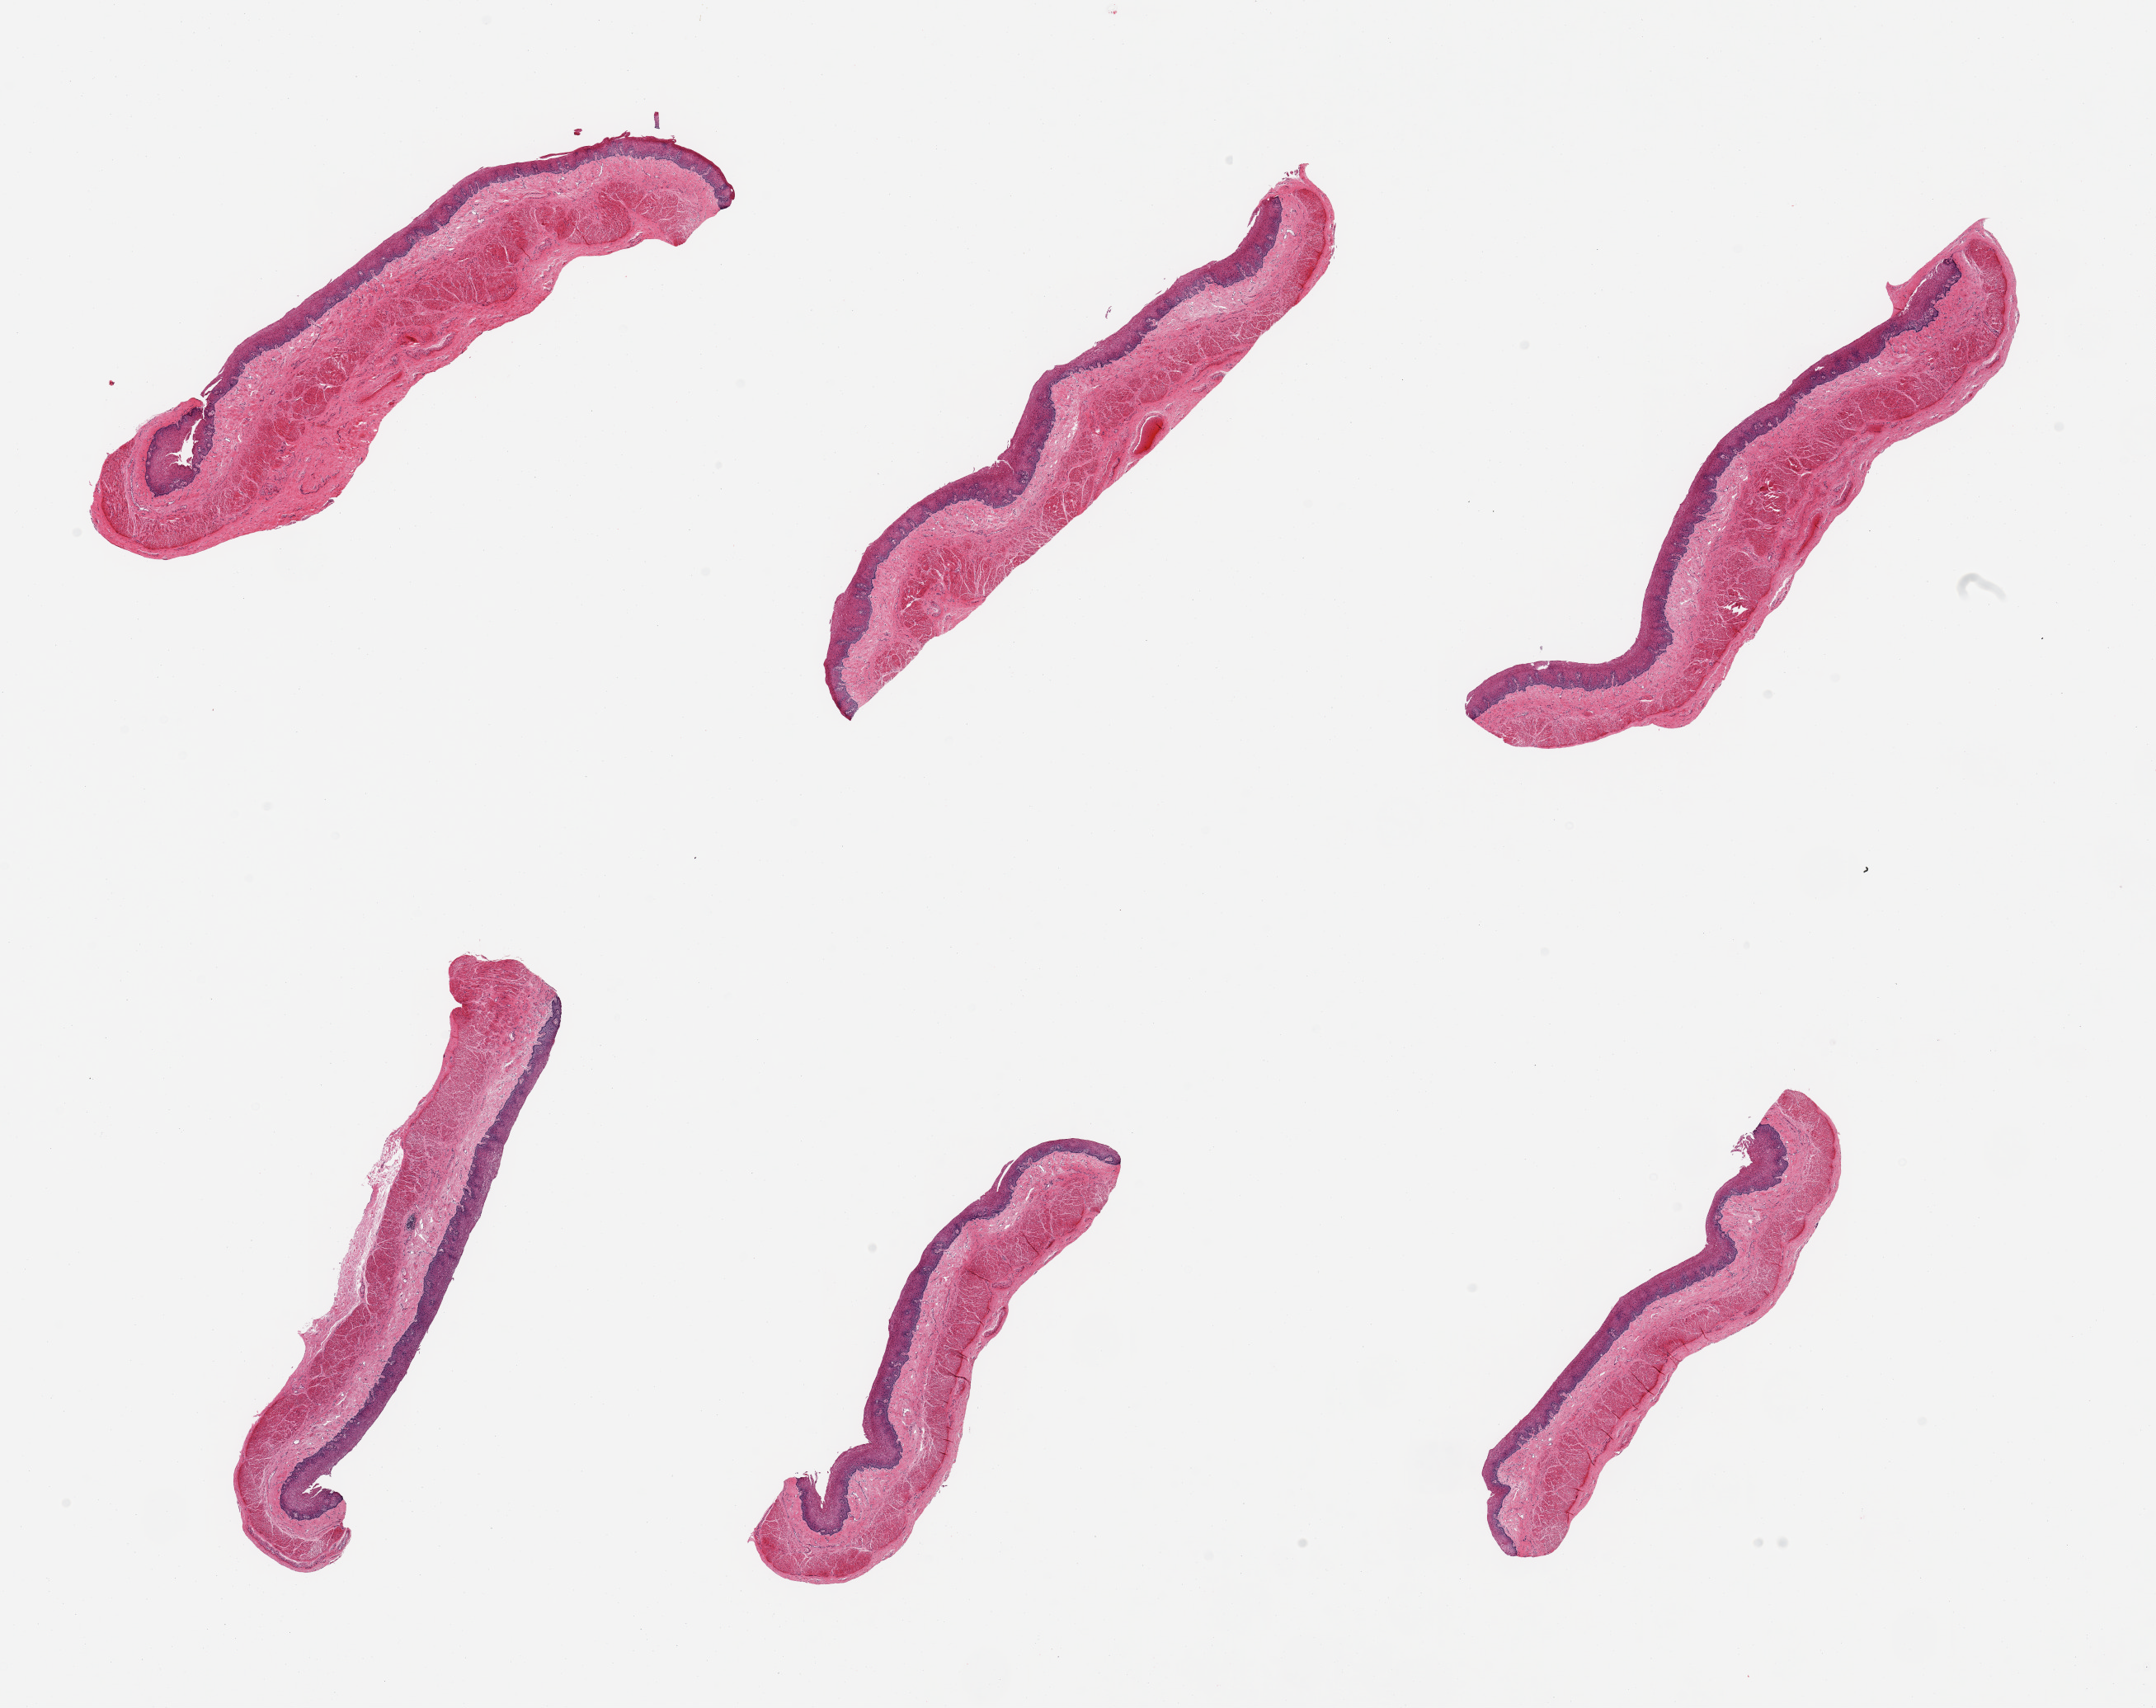
Digitized haematoxylin and eosin-stained section — whole scanned area (about 20.7 x 16.4 mm) shown as a low-resolution overview. PAXgene-fixed, paraffin-embedded tissue. Sampled site (target tissue): esophageal mucous membrane. Donor tissue sample. Donor: female.
- reviewer comment on this tissue sample: 6 pieces; well dissected; no submucosal glands